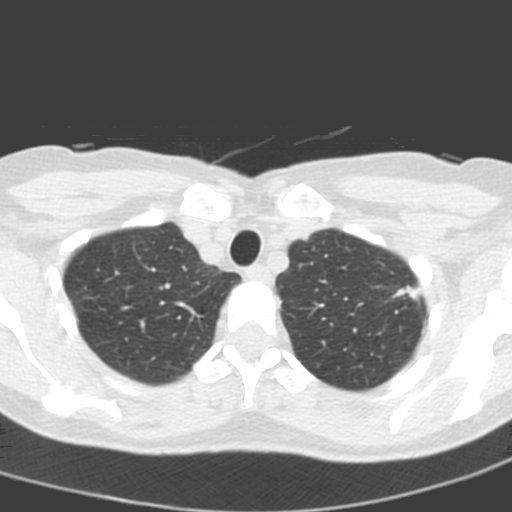
Low-dose screening chest CT, one axial slice. Position 164 of 193 along the scan axis. 120 kVp. Lung window (W 1500 / L -600 HU). 3.2 mm slice thickness. 512 × 512 image matrix.
Structures marked on this image (expert manual segmentation):
- lesion 1 (tumor, upper lobe of left lung): bounding box <393,286,421,301> (left, top, right, bottom; pixels)